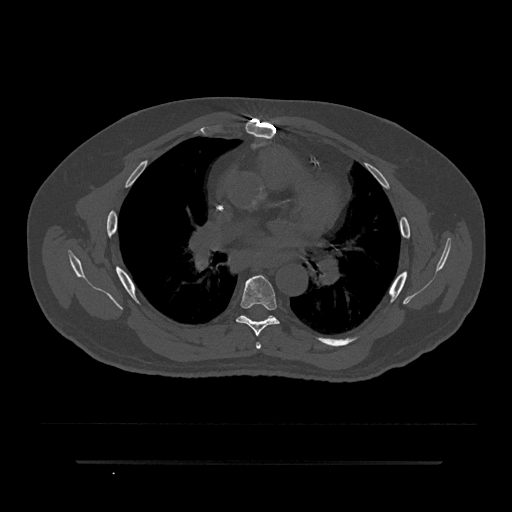
CT including the spine, one axial slice. Slice 523 of 797 in the series (ordered by position). Reconstruction kernel Br40s/3. Bone window (W 1800 / L 400 HU). 512 × 512 image matrix, field of view 464 × 464 mm. Patient: male, 59 years. From the clinical record (not read from this slice): primary cancer: bile ducts; vertebrae with lytic lesions (as recorded): T10.
Structures marked on this image (semi-automatically segmented with operator editing):
- T5 vertebra: bounding box <256,342,261,349> (left, top, right, bottom; pixels)
- T6 vertebra: <236,275,280,336>